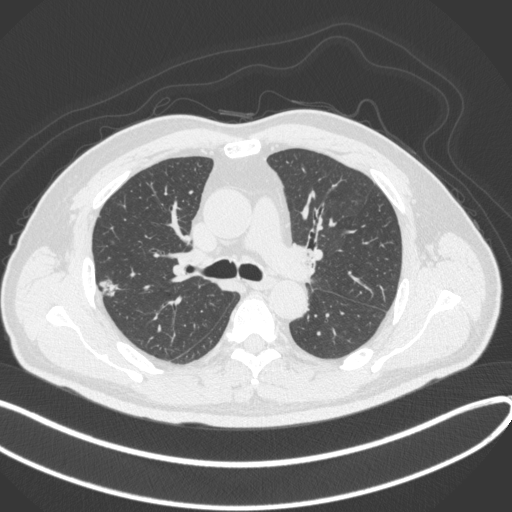
Chest CT, one axial slice. Reconstruction kernel B31f. Lung window (W 1500 / L -600 HU). 1 mm slice thickness. 512 × 512 image matrix, field of view 400 × 400 mm. Male patient, age 60 years. From the clinical record (not read from this slice): clinical TNM (as recorded): T1c N0 M0.
Structures marked on this image (rectangle marked by the reading radiologist):
- lung tumour (recorded histology: adenocarcinoma): bounding box [x1, y1, x2, y2] px = [94, 271, 123, 303]